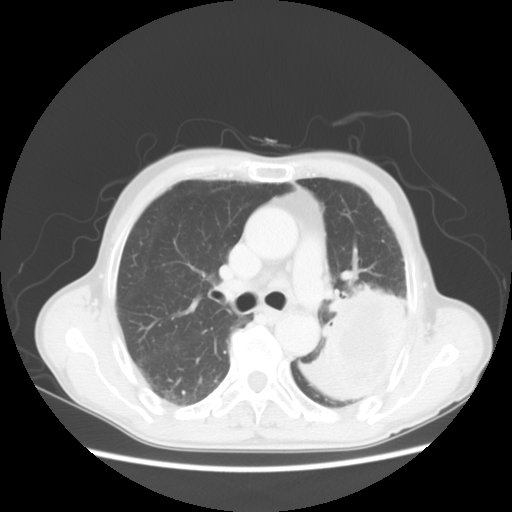
Chest CT, one axial slice; slice 33 of 51 in the series (ordered by position); 120 kVp; lung window (W 1500 / L -600 HU); 5 mm slice thickness; 512 × 512 image matrix, field of view 360 × 360 mm. Male patient, age 64 years. From the clinical record (not read from this slice): clinical TNM (as recorded): T4 N0 M0.
Annotated regions visible in this slice (bounding box drawn by a radiologist):
- lung tumour (recorded histology: squamous cell carcinoma): box from (x=311, y=276) to (x=419, y=415) px